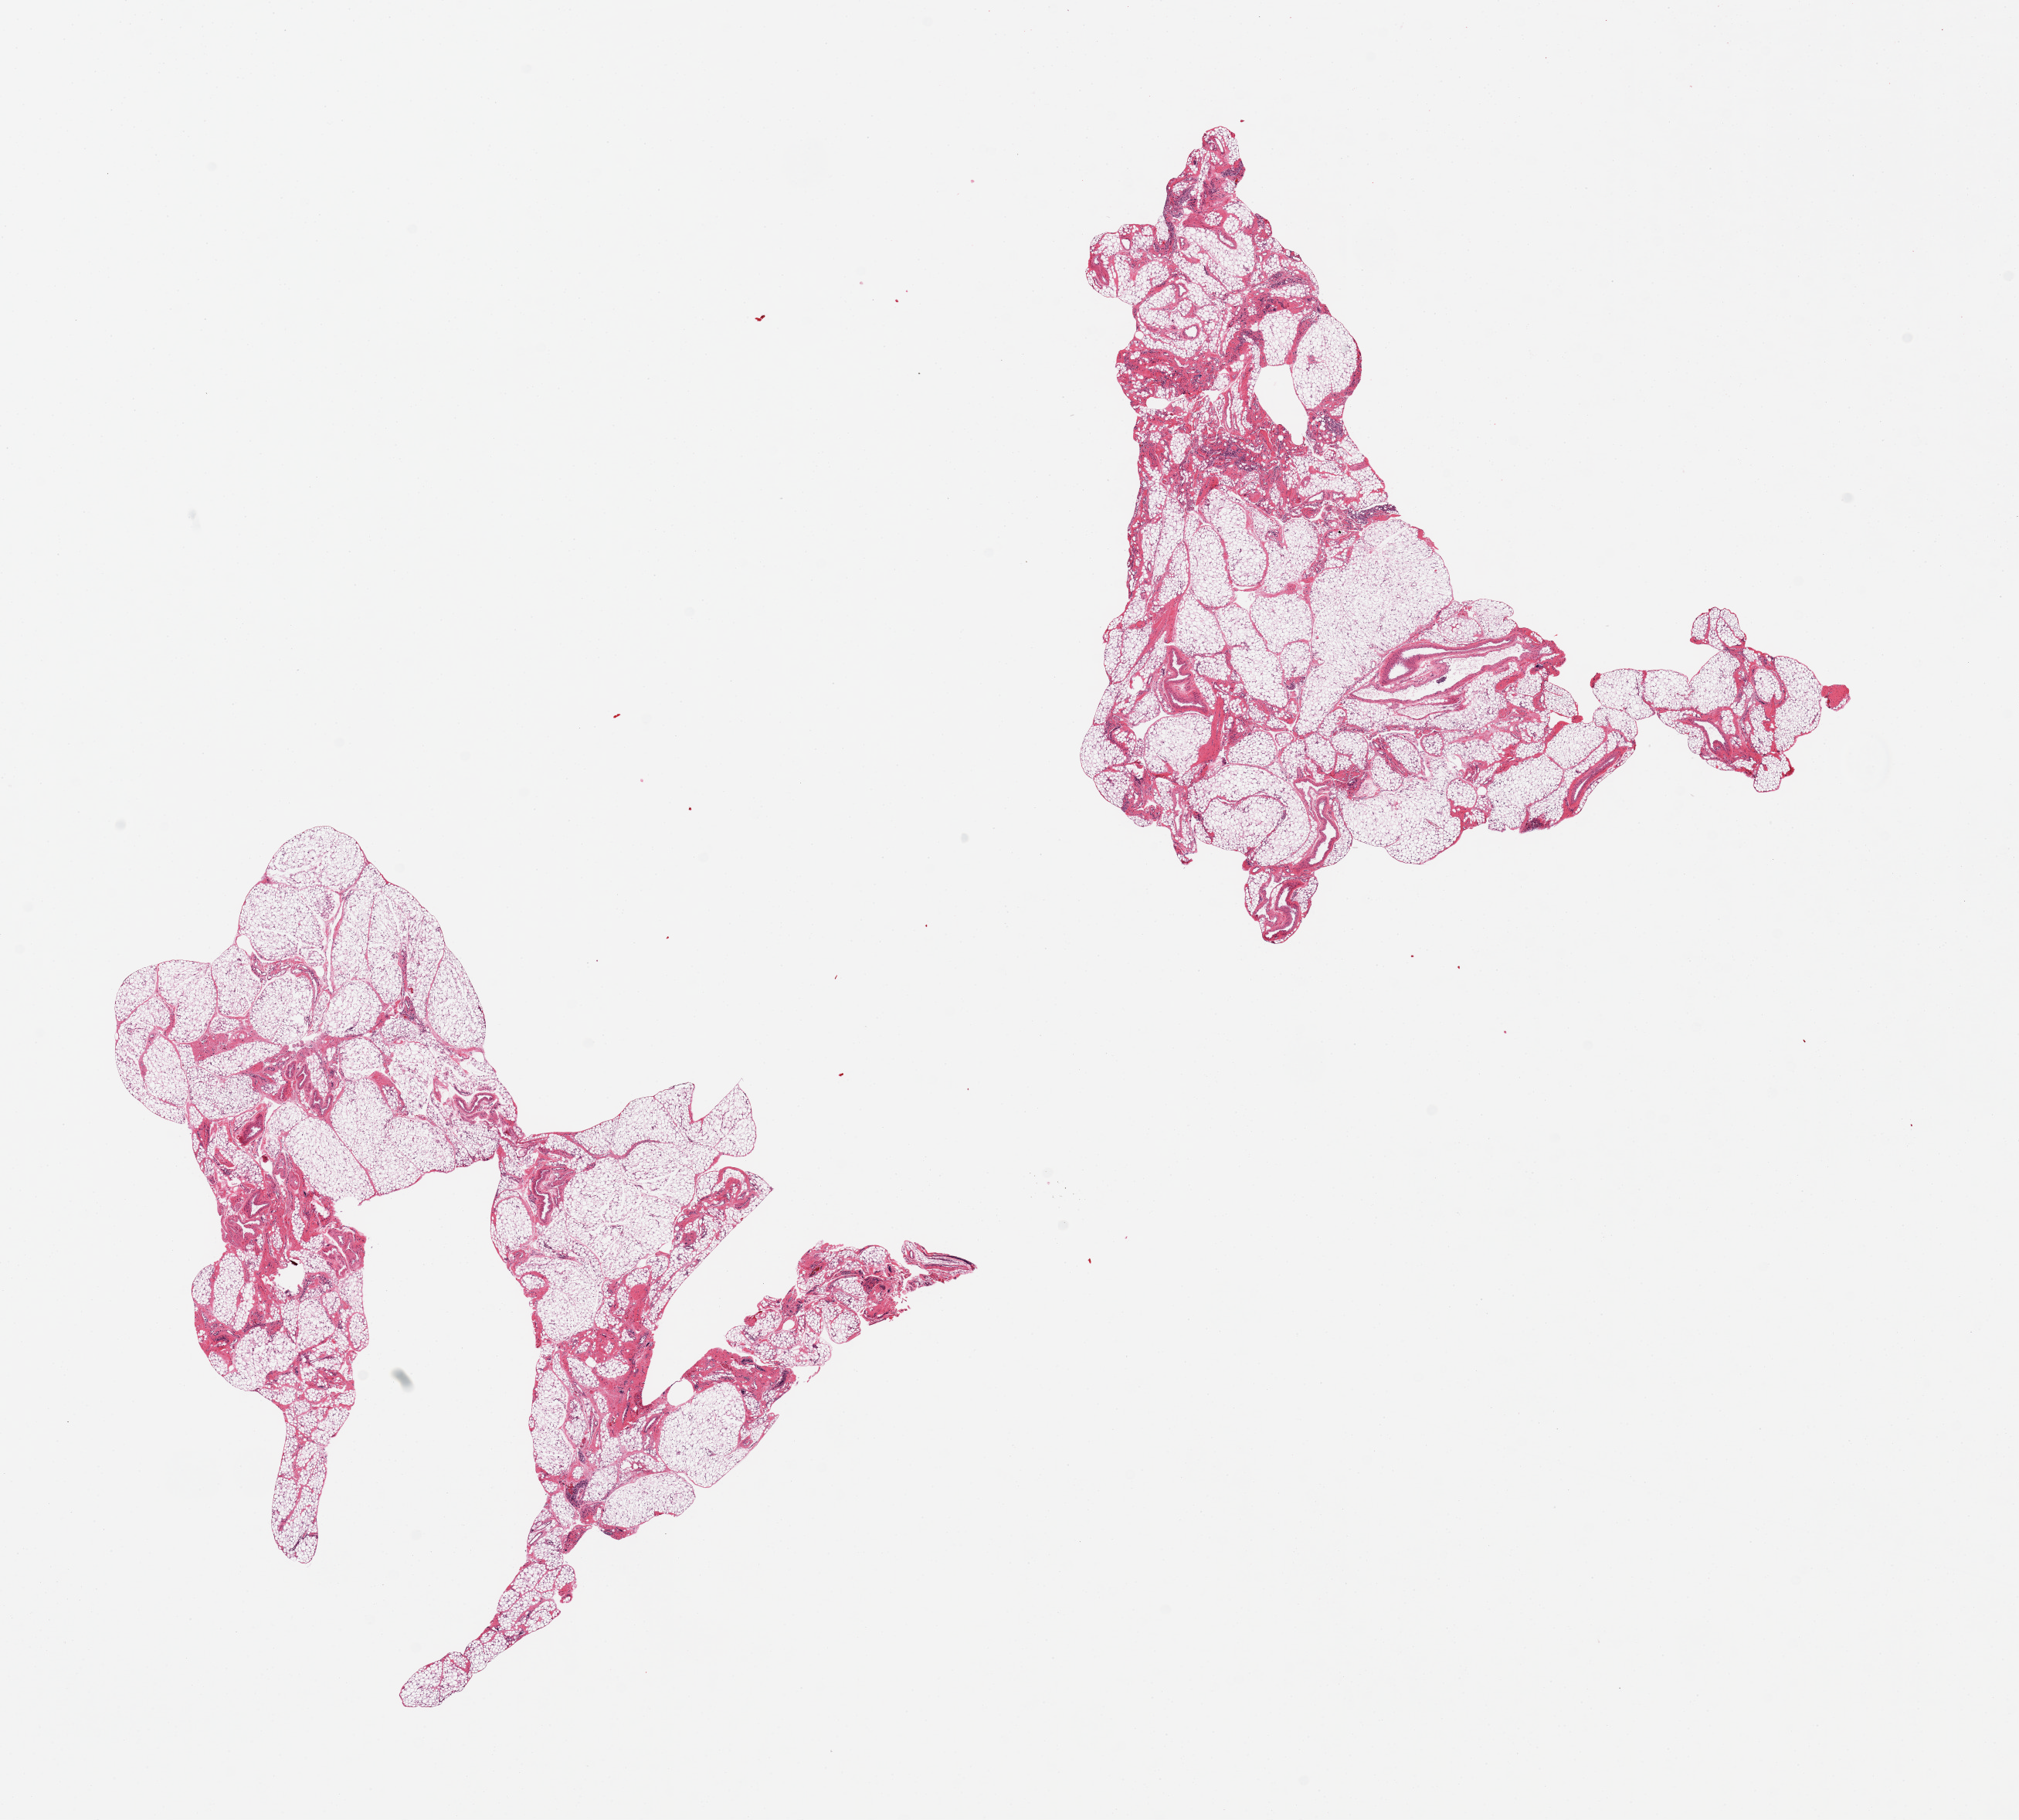
H&E whole-slide image, whole scanned area (about 20.7 x 18.6 mm, slide scanned at 20x) shown as a low-resolution overview. PAXgene-fixed paraffin-embedded (PFPE) section. Sampled site (target tissue): omentum. Donor tissue sample.
- reviewer comment on this tissue sample: 2 pieces